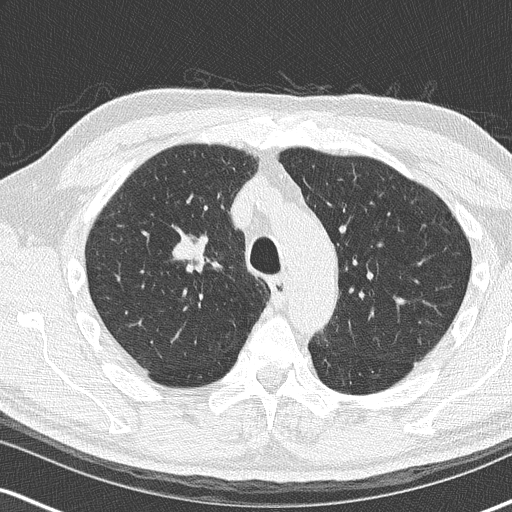
Low-dose screening chest CT, axial slice, second screening round (one year after baseline), lung window (W 1500 / L -600 HU), 2 mm slice thickness, lung (sharp) reconstruction kernel (B50f). Male participant, aged 68 years at enrolment. Current smoker at enrolment.
Expert-annotated lung lesion, bounding box <152,226,217,288> (left, top, right, bottom; pixels). The exam's reader record, not a measurement of the box and not confirmed to be the same lesion: non-calcified nodule or mass ≥4 mm, right upper lobe, 18 × 15 mm, smooth margins, soft tissue attenuation, pre-existing on the prior screen: no. Later outcome: lung cancer diagnosed 136 days after this screen — small cell carcinoma, NOS, right upper lobe, stage IIIB (AJCC 6th edition), 20 mm at pathology.